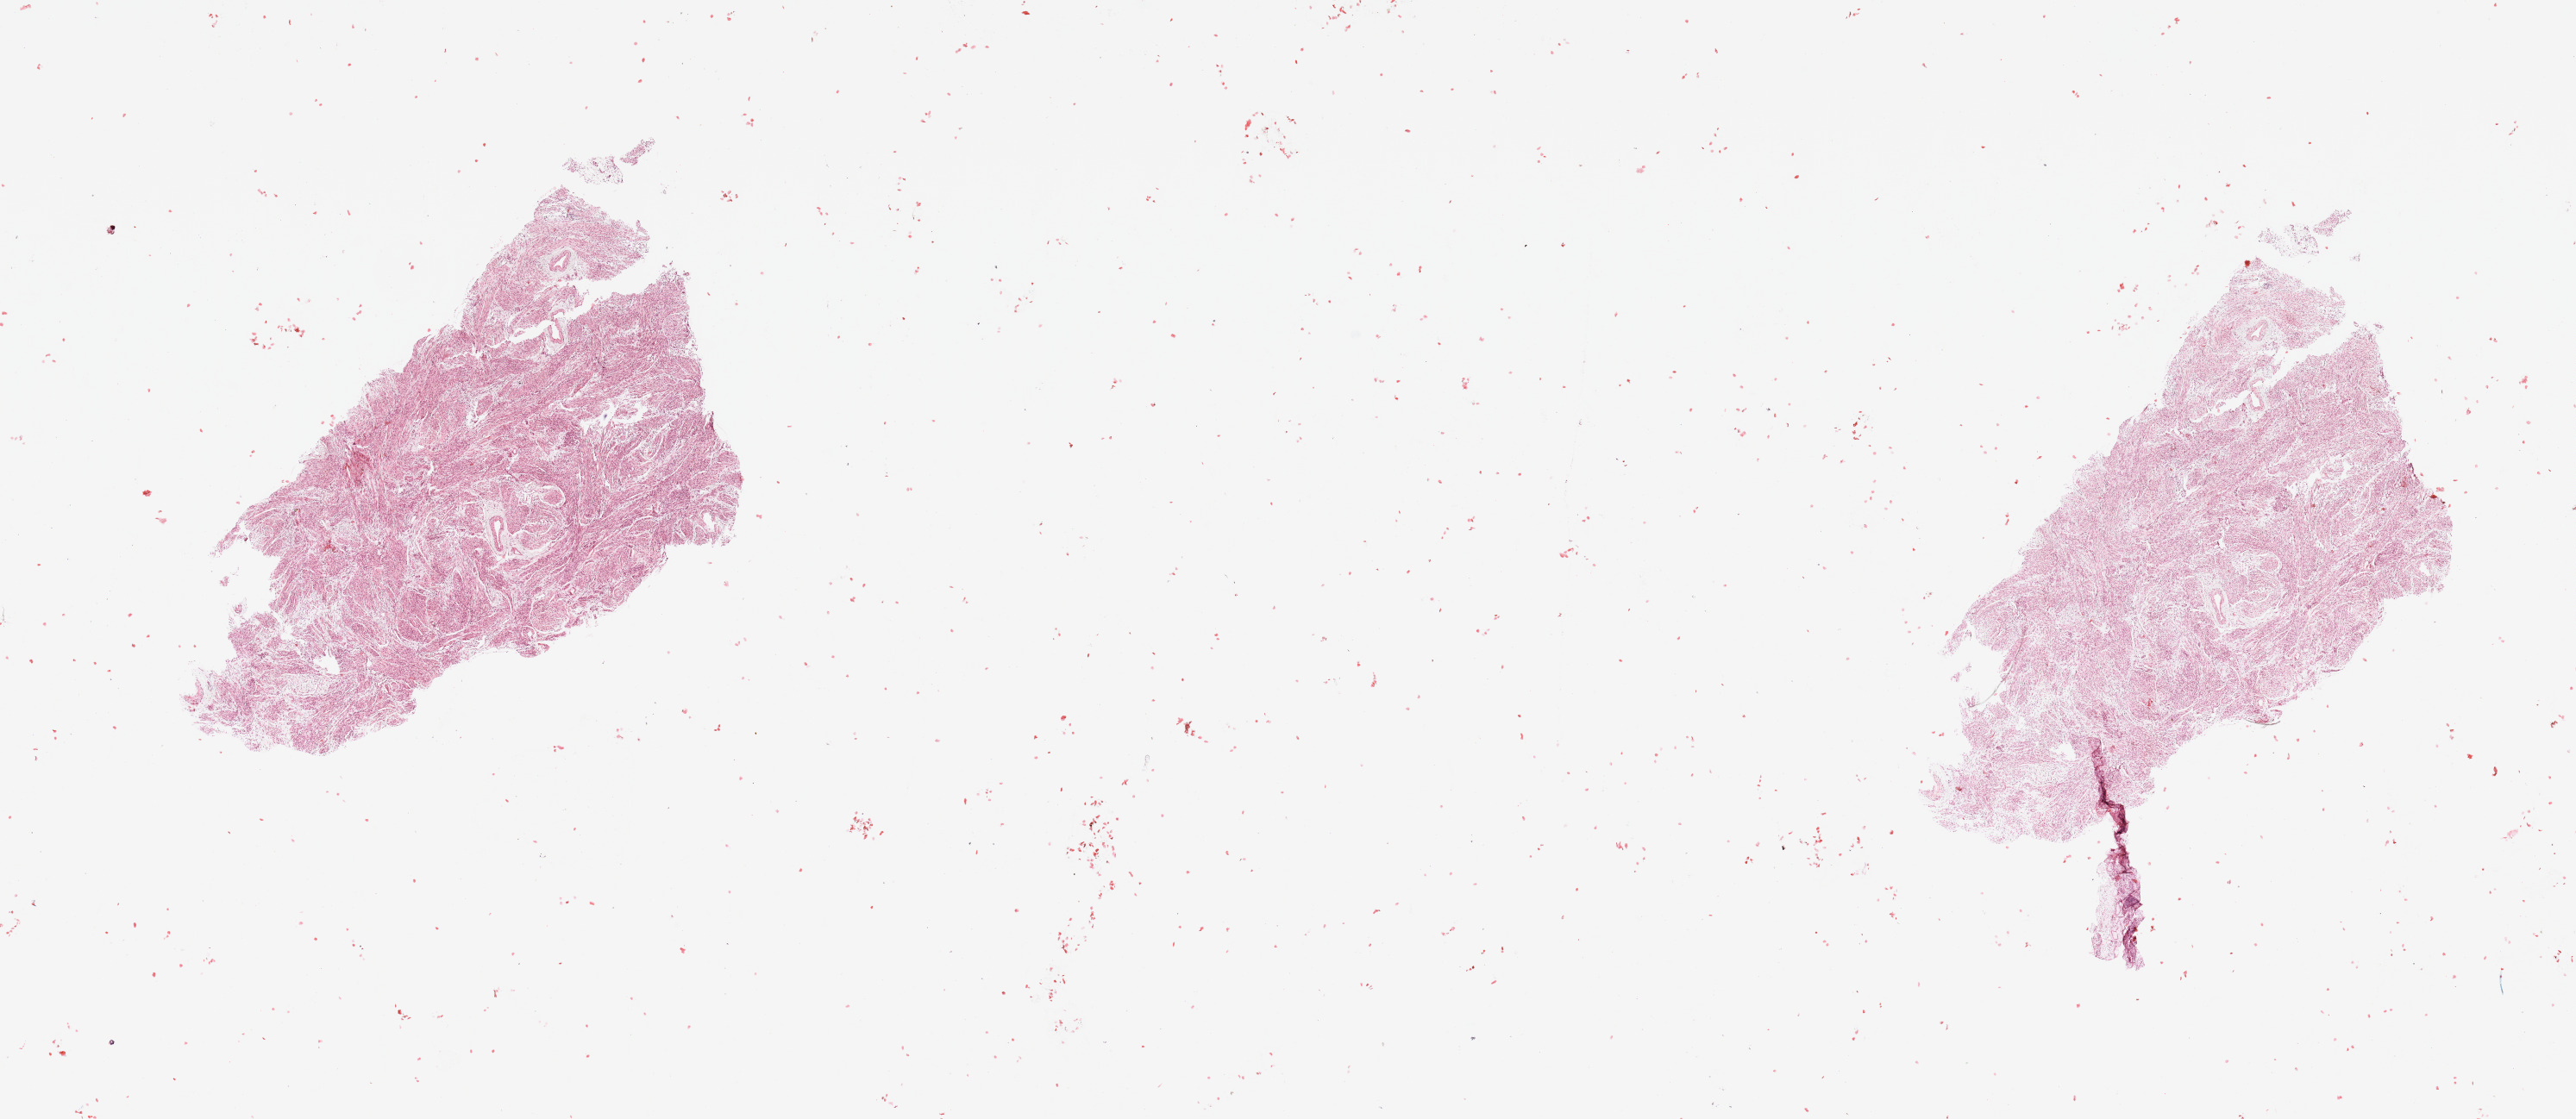
H&E whole-slide image, shown as a low-resolution overview of the whole scanned area (about 23.6 x 10.3 mm, acquisition: 20x scan). Normal (non-tumour) tissue sample, sampled site: uterus. Female, 68 y/o.
This section: normal (non-tumour) tissue from the same patient. Patient diagnosis: Endometrioid adenocarcinoma, NOS.